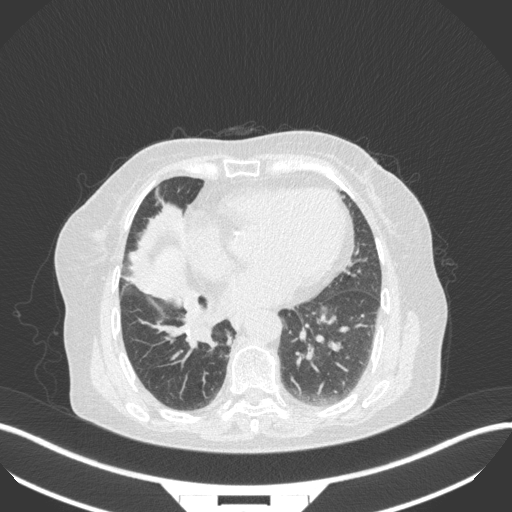
Chest CT, one axial slice; slice 119 of 329 in the series (ordered by position); lung window (W 1500 / L -600 HU); 512 × 512 image matrix, field of view 400 × 400 mm. Female patient, age 75 years. Case-level facts recorded for this patient, not image findings: clinical TNM (as recorded): T1b N0 M1a; histopathological grade: G1.
Annotated regions visible in this slice (bounding box drawn by a radiologist):
- lung tumour (recorded histology: squamous cell carcinoma): bounding box <181,304,218,349> (left, top, right, bottom; pixels)